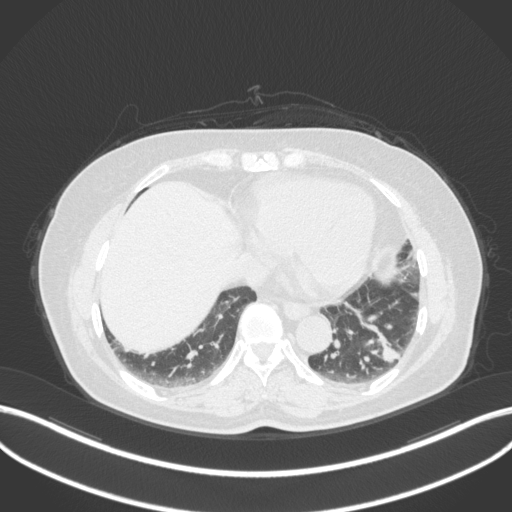
Chest CT, one axial slice. Position 117 of 307 along the scan axis. Lung window (W 1500 / L -600 HU). 1 mm slice thickness. 512 × 512 image matrix. Female patient, age 59 years. Case-level facts recorded for this patient, not image findings: clinical TNM (as recorded): T2a N0 M0; histopathological grade: G2-3.
Annotated regions visible in this slice (rectangle marked by the reading radiologist):
- lung tumour (recorded histology: adenocarcinoma): box from (x=354, y=319) to (x=400, y=365) px